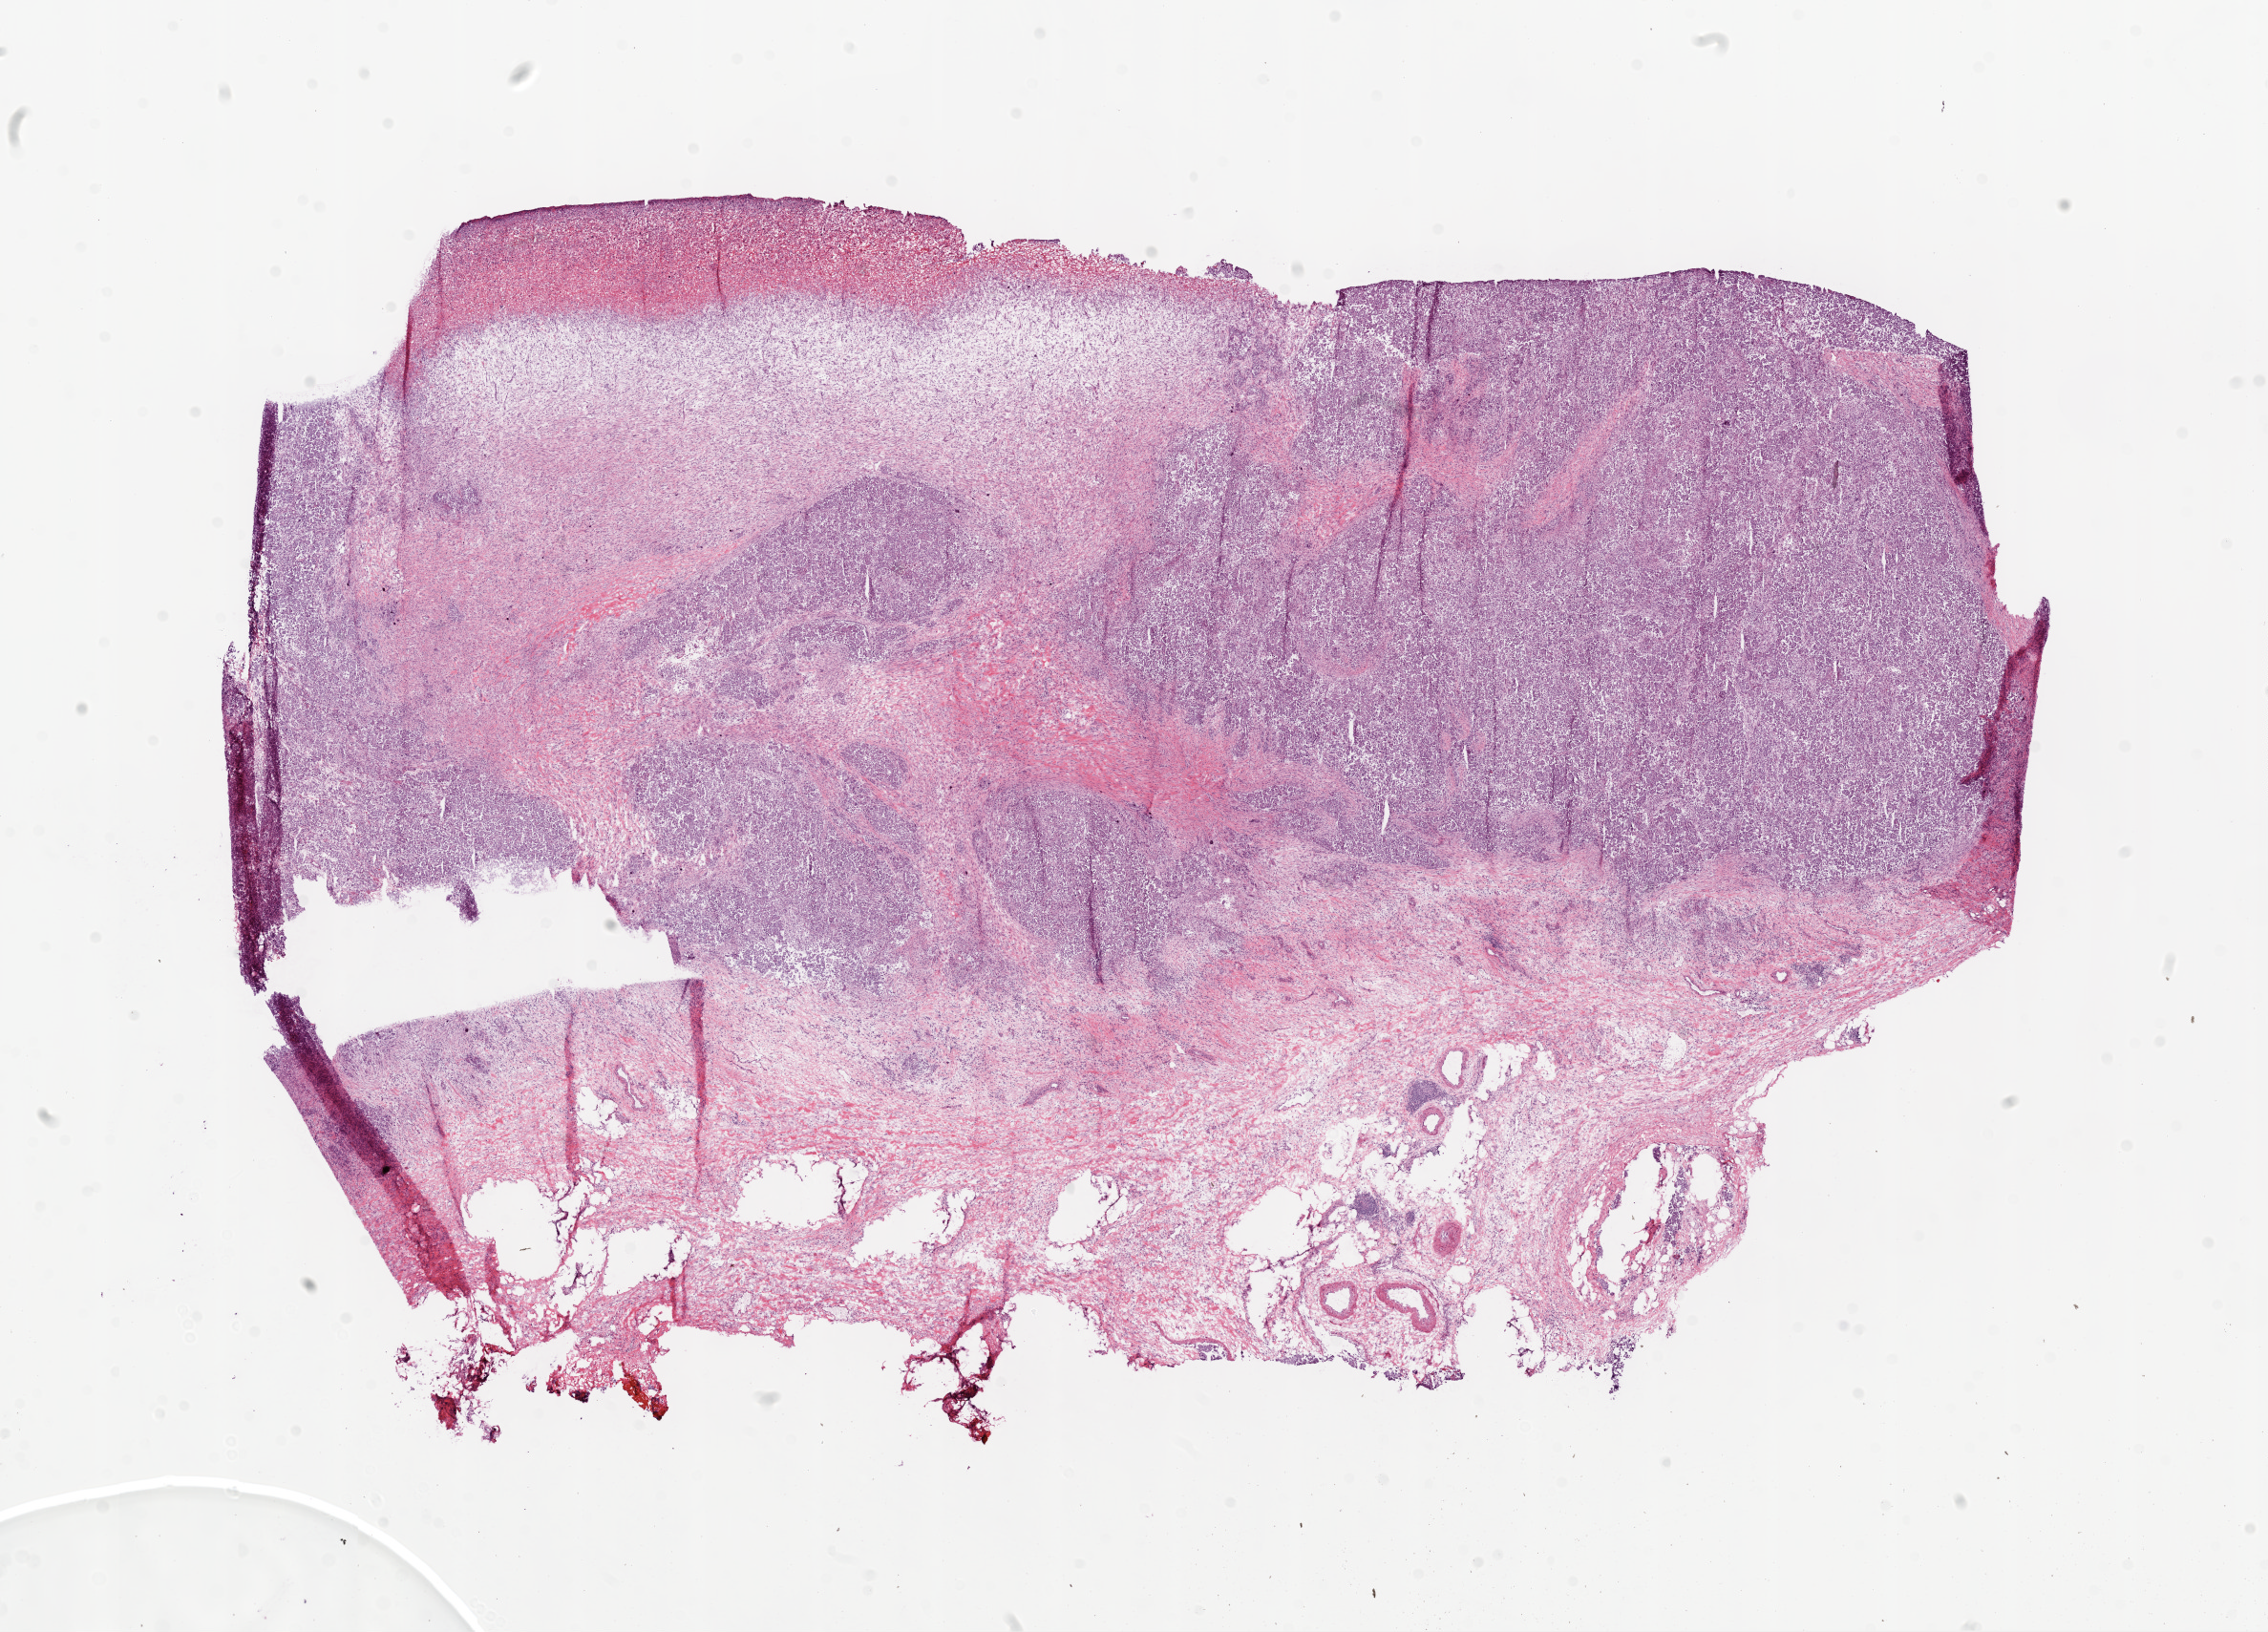
Whole-slide histology image, H&E-stained — whole scanned area (about 19.1 x 13.7 mm) shown as a low-resolution overview. Frozen section from the bottom of the tissue portion. Sample: primary tumour, ovary. Patient: female, age at initial diagnosis 64 years. Histologic grade: G3 (poorly differentiated). Composition of this section per pathologist review: tumour cells 75%, tumour nuclei 80%, normal cells 1%, stromal cells 19%, necrosis 5%.
Laterality: bilateral. FIGO stage: IIIC. Pathologic diagnosis: Serous cystadenocarcinoma, NOS.